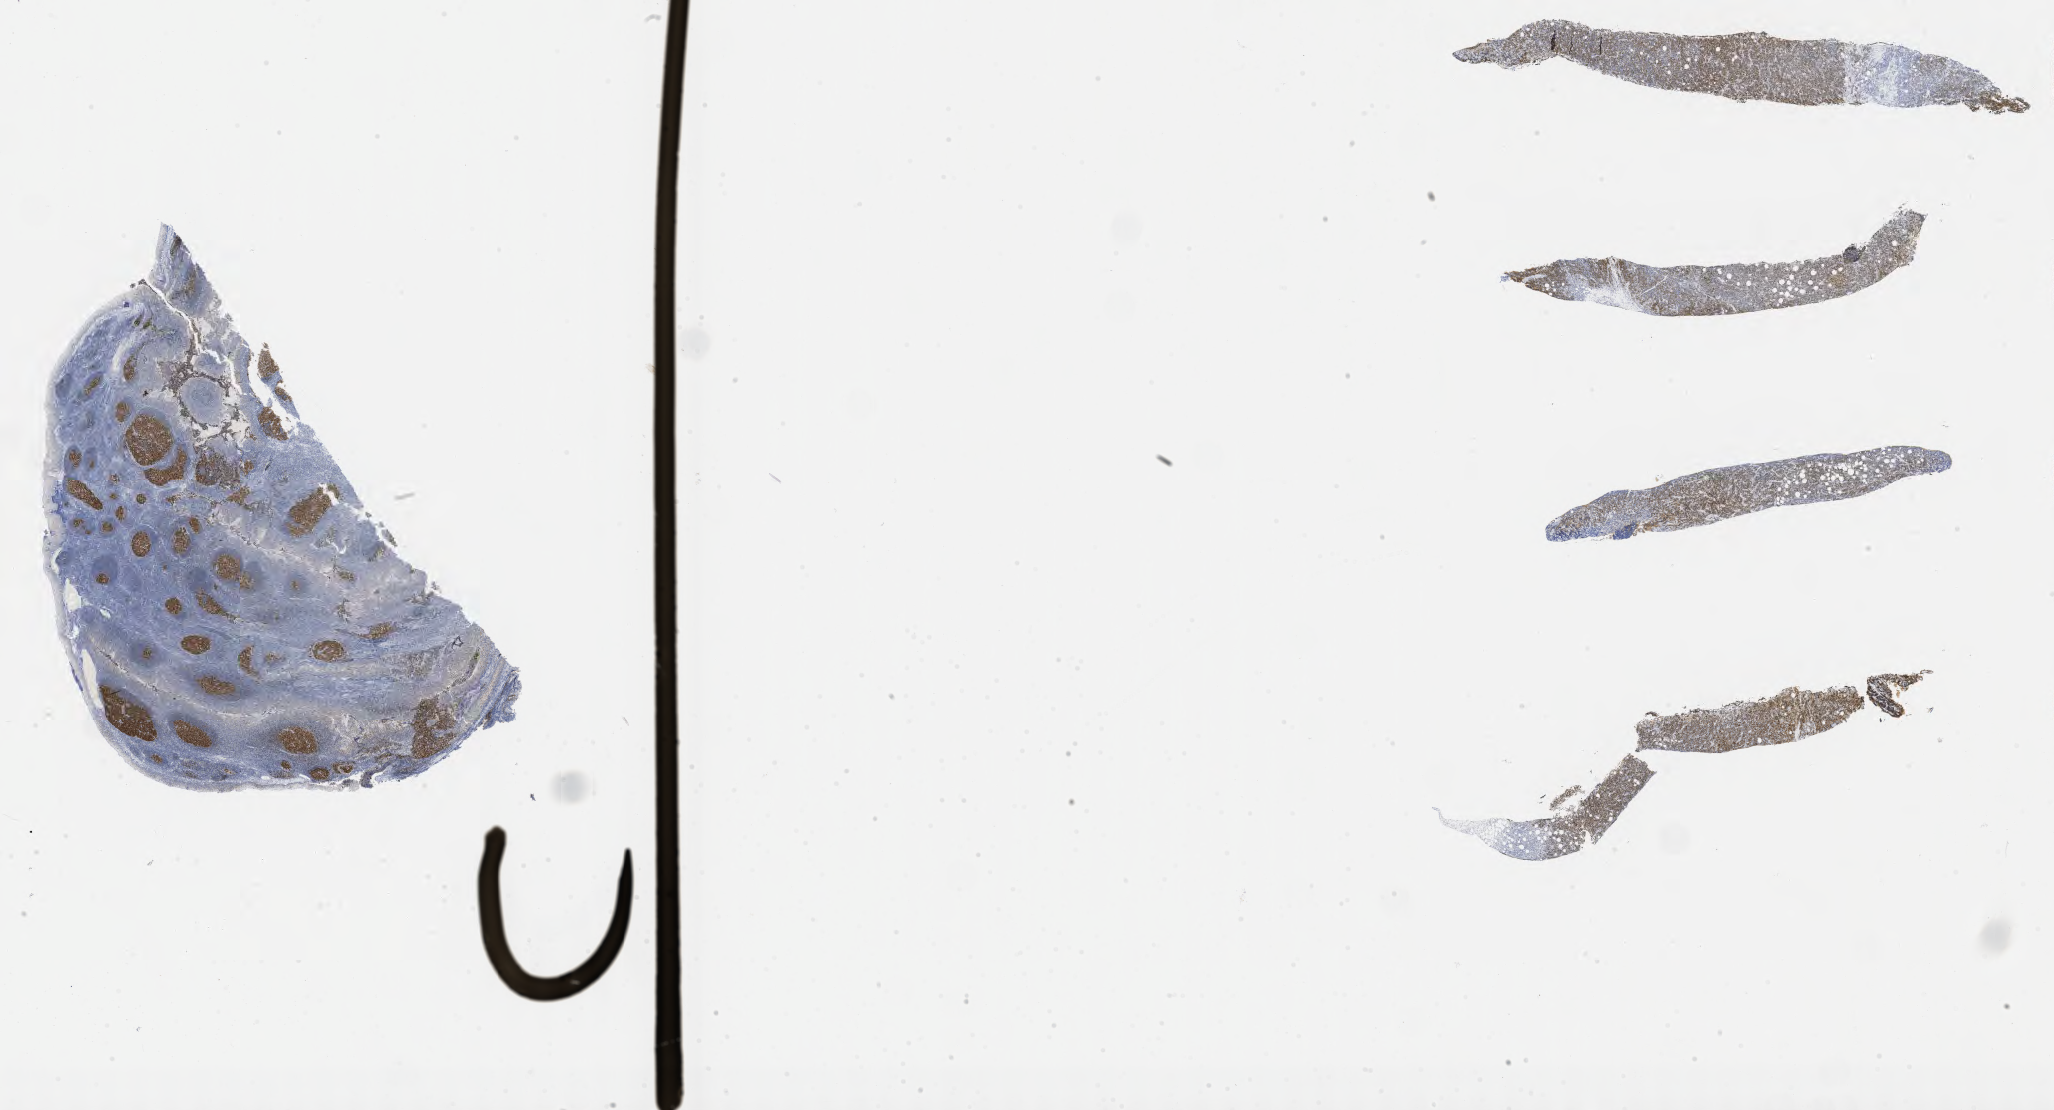
Immunohistochemistry (IHC) whole-slide image stained for BCL6, whole scanned area (about 33.2 x 18.0 mm) shown as a low-resolution overview, tumor tissue. Patient: male, 69 years old.
Diagnosis: Diffuse large B-cell lymphoma, NOS.